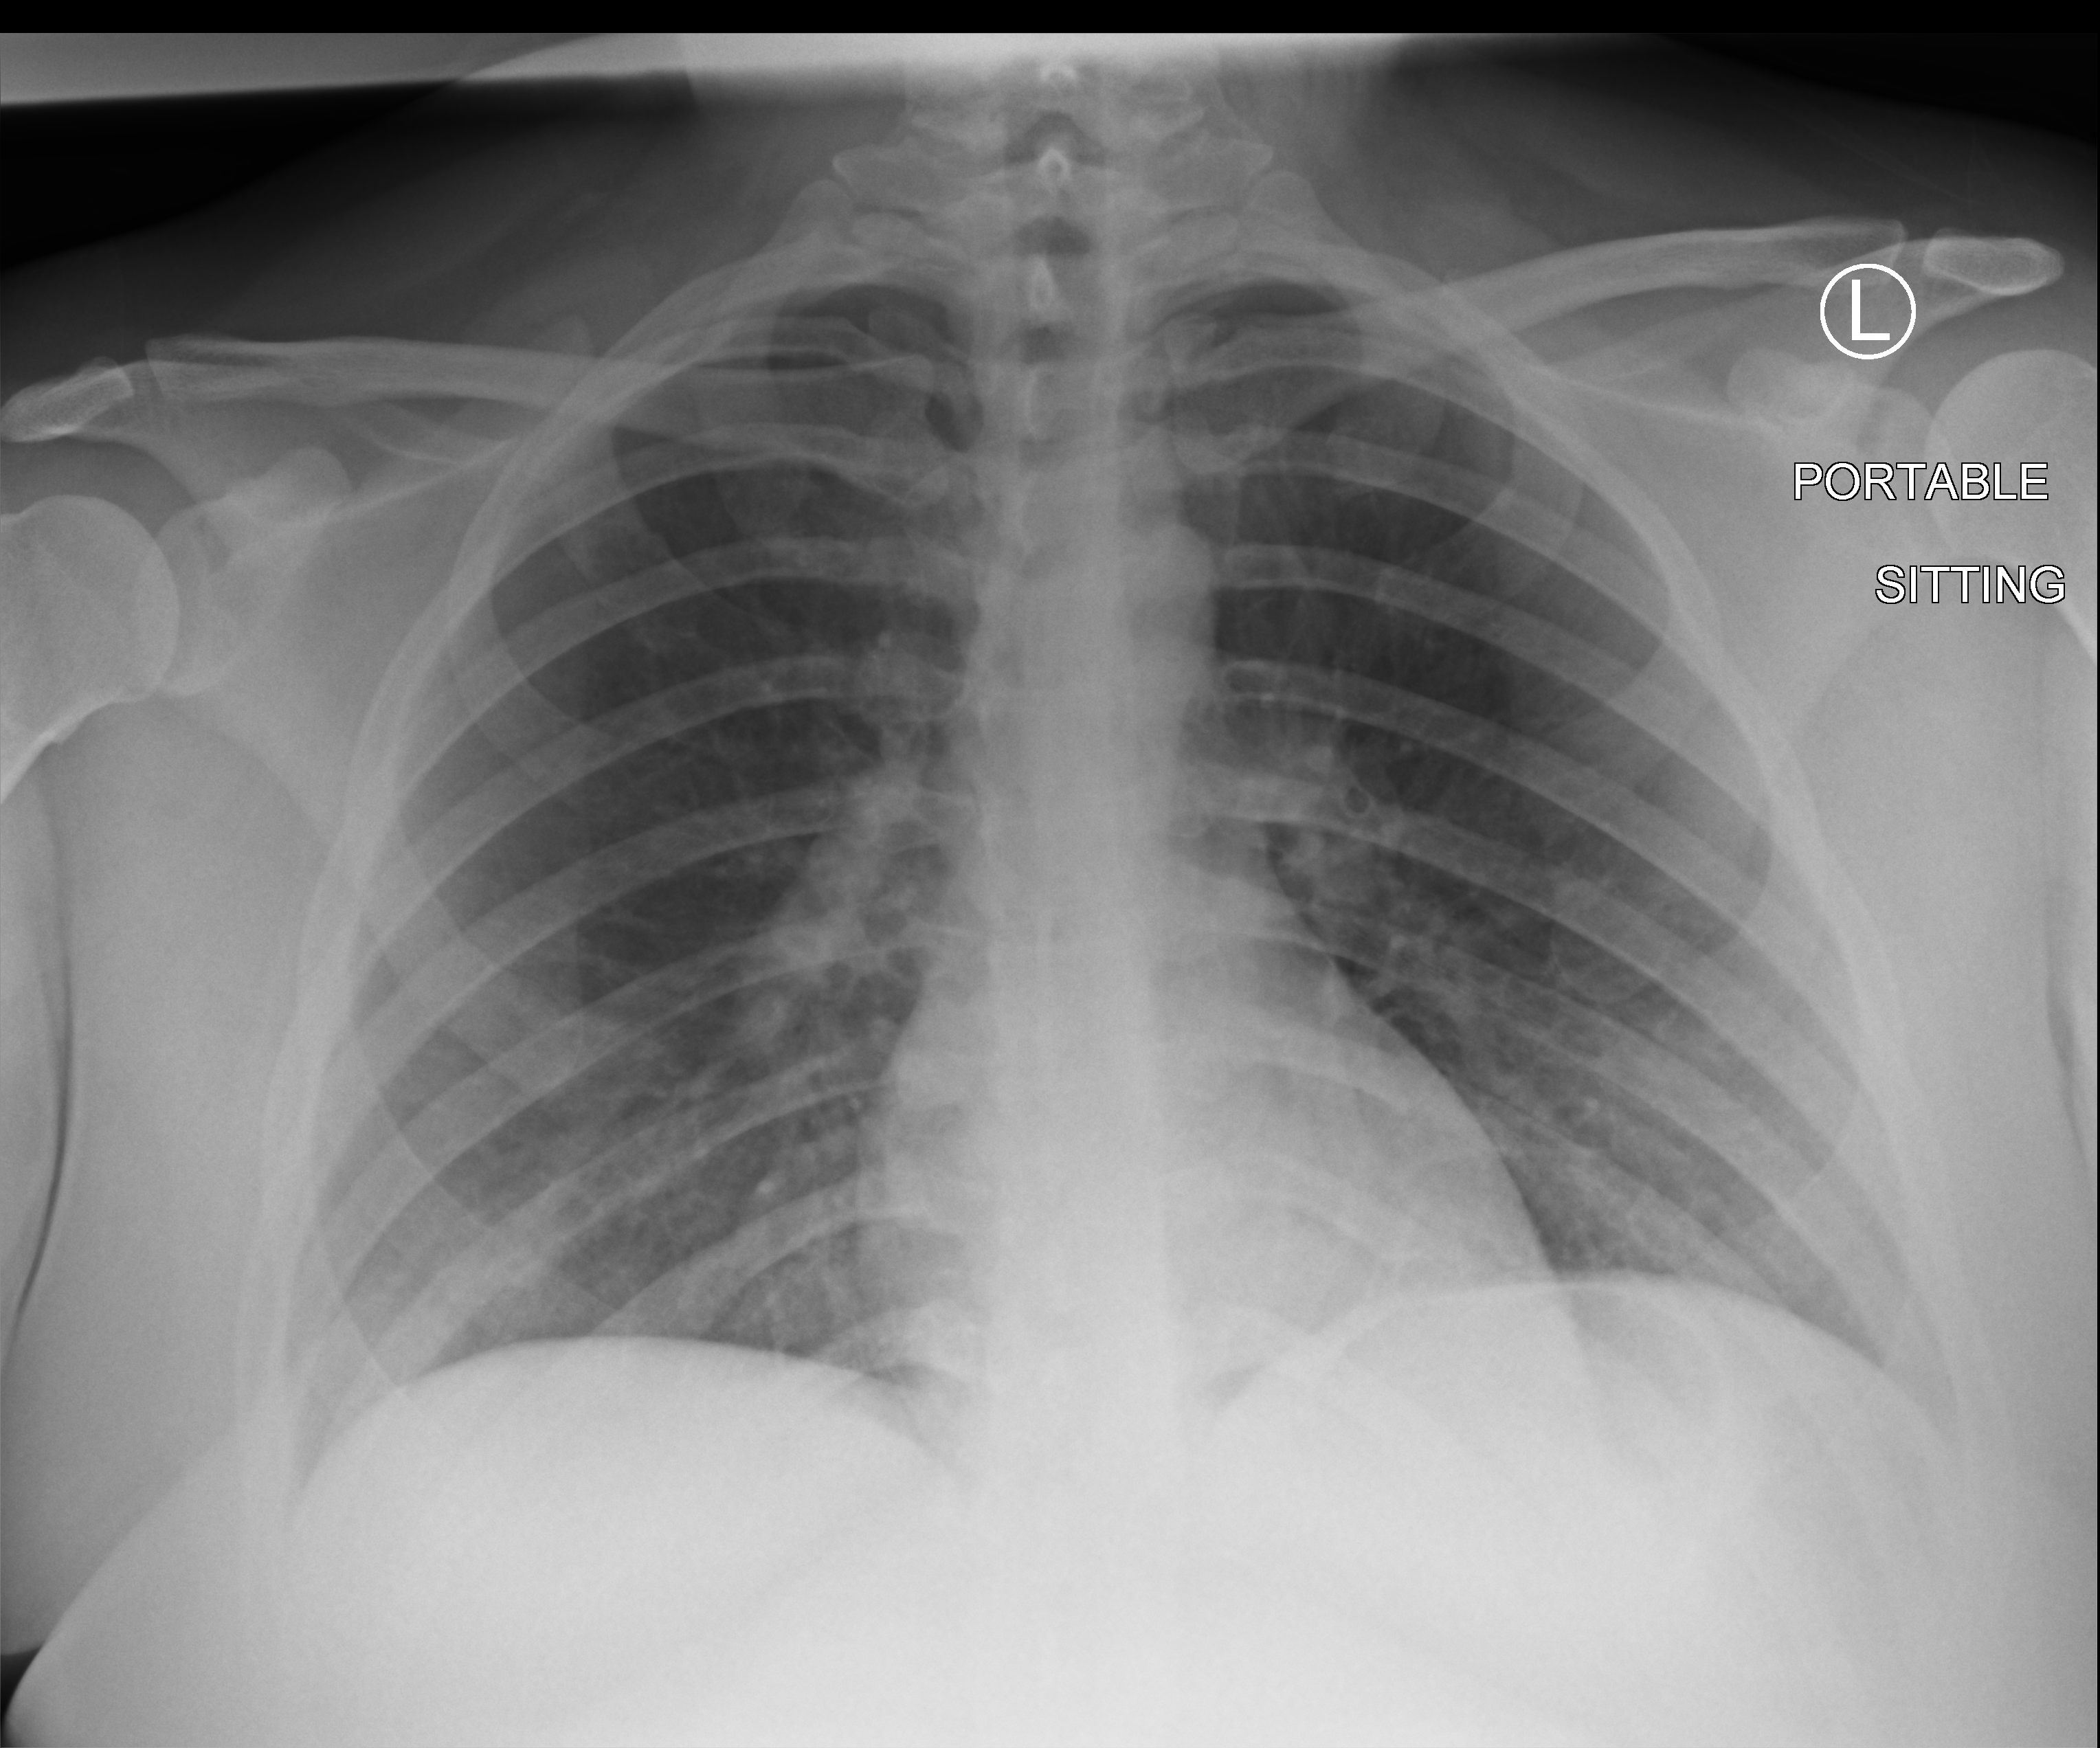
Chest X-ray (portable). Female patient hospitalised with COVID-19, age 18–59 years.
Hospital-stay facts (about this admission, not read from this image; timing relative to this image not recorded): admitted to intensive care during this hospital stay: no; mechanically ventilated during this hospital stay: no.